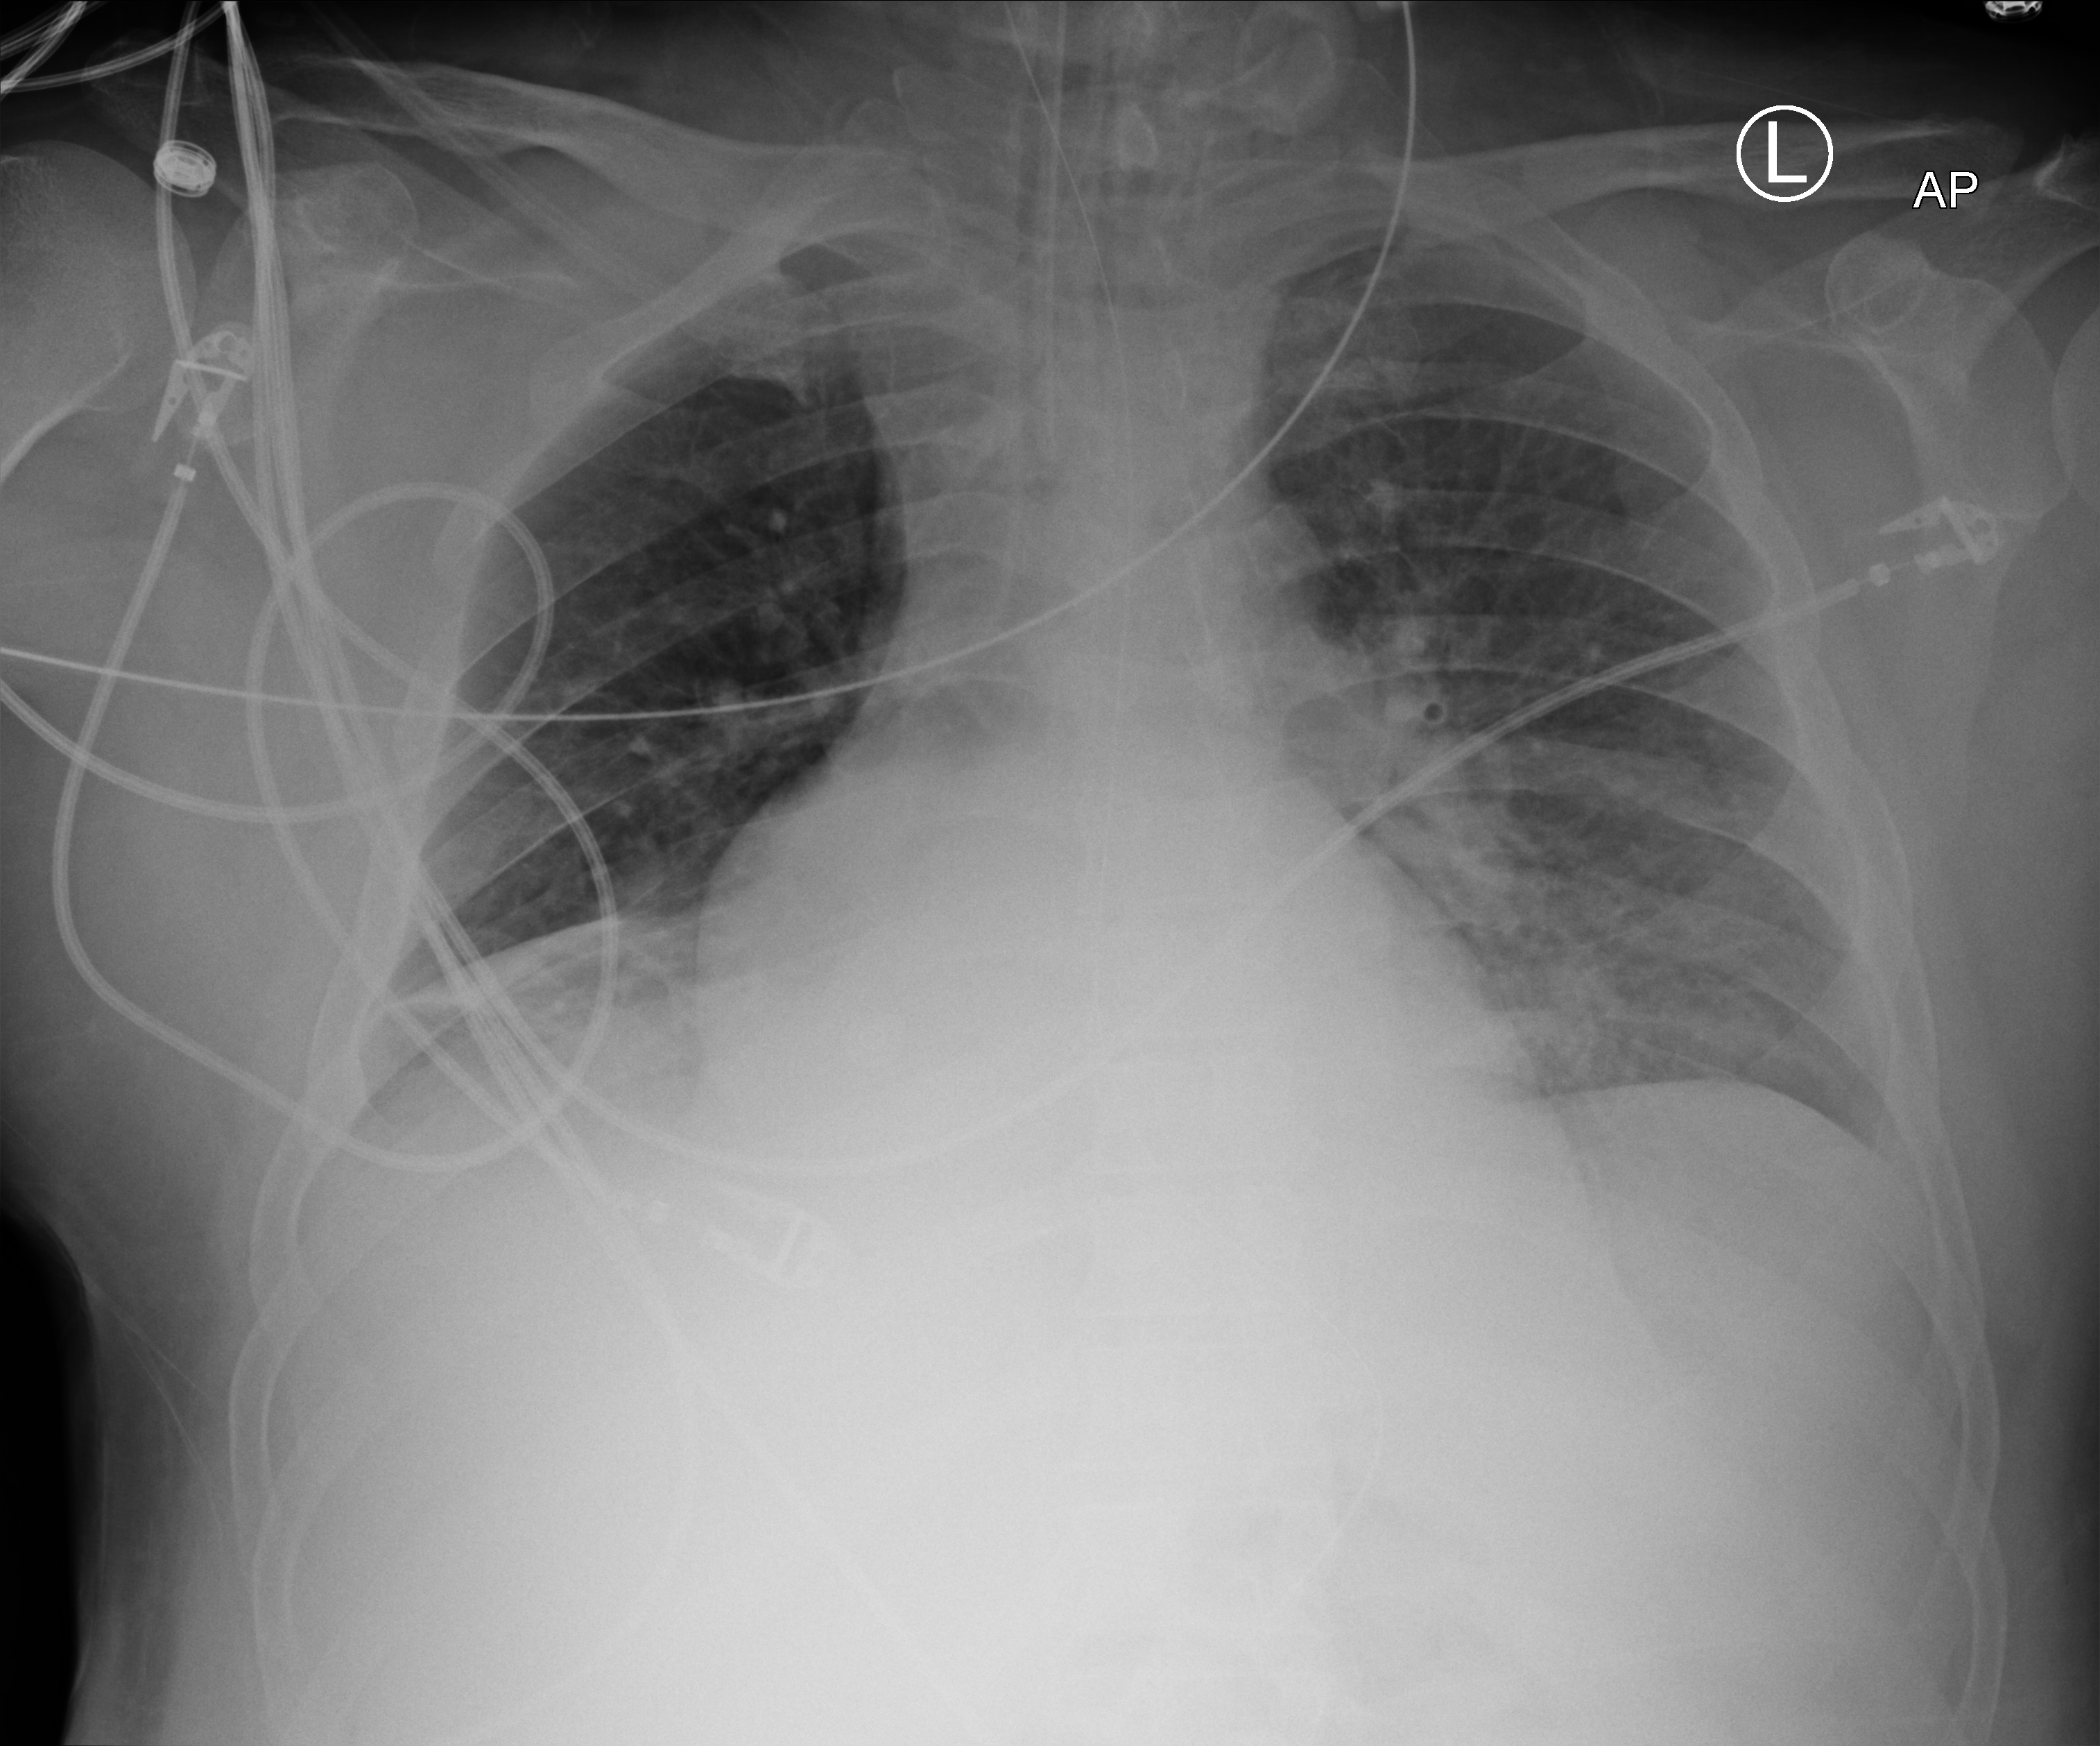
Portable chest radiograph; anteroposterior (AP) projection. Male patient hospitalised with COVID-19, age 18–59 years.
From the hospital-stay record, not from the radiograph (when in the stay this image was taken is not recorded): admitted to intensive care during this hospital stay: yes; mechanically ventilated during this hospital stay: yes.